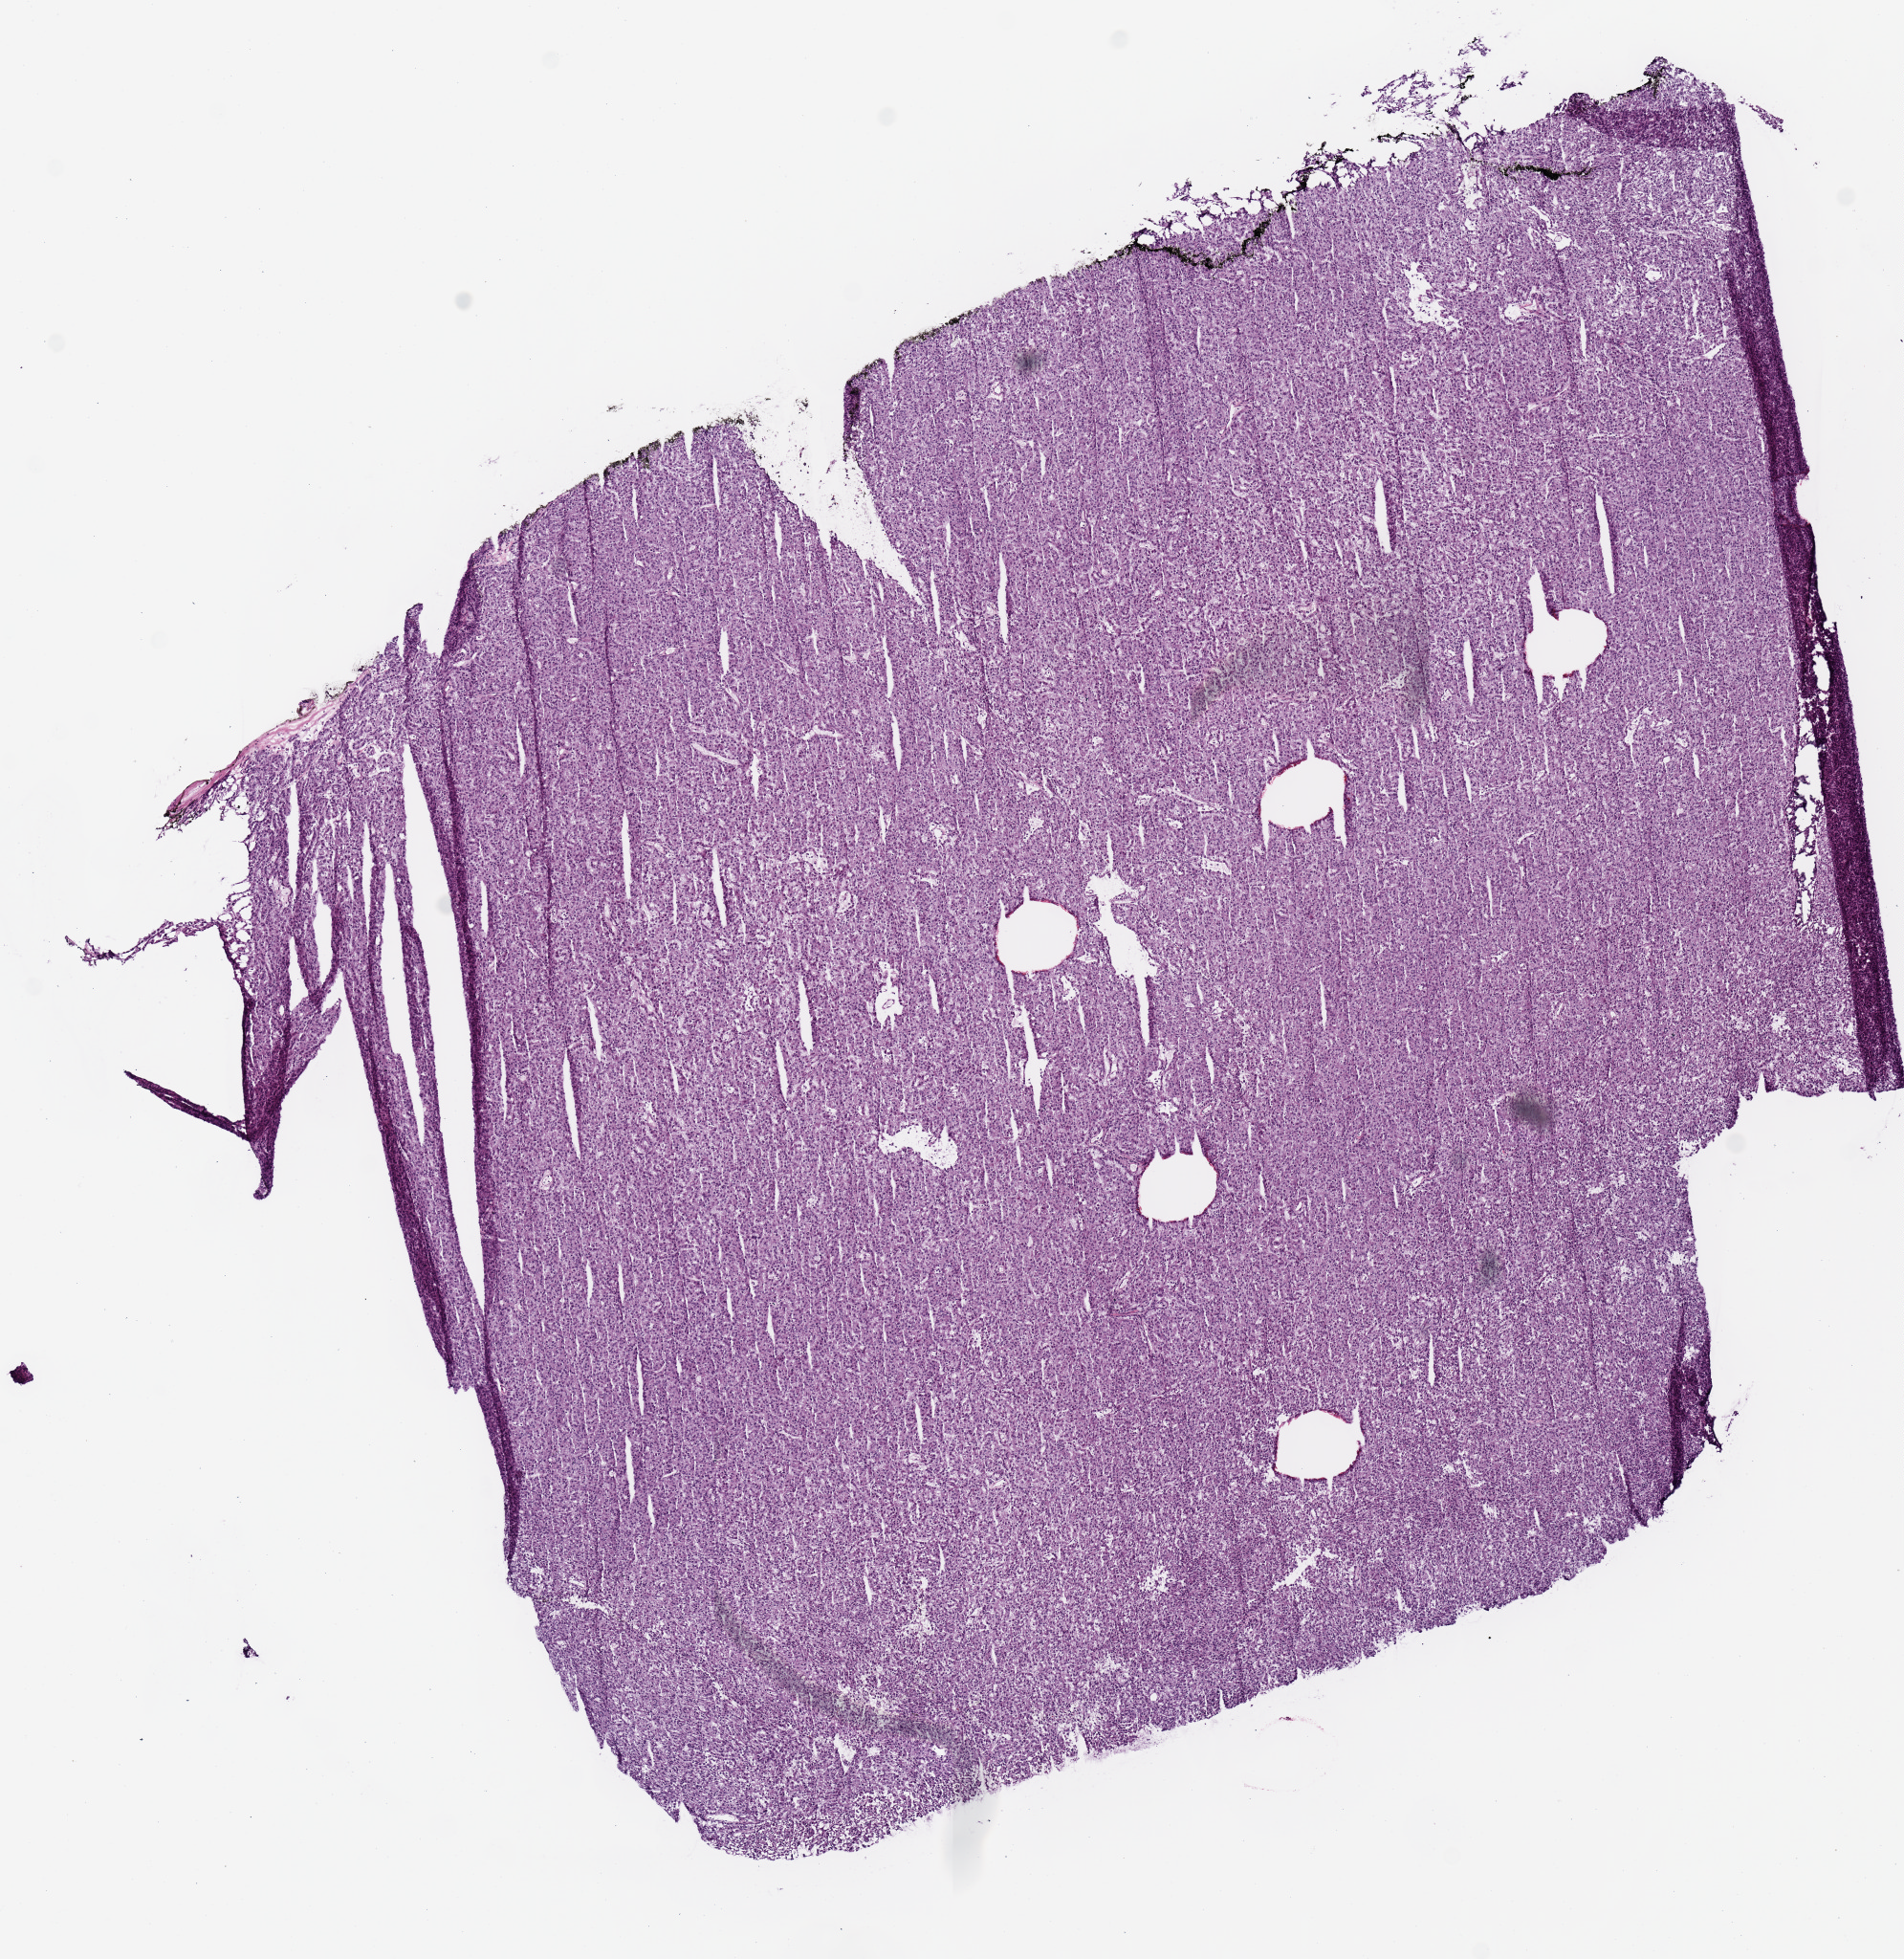
H&E-stained whole-slide image — whole scanned area (about 7.9 x 8.1 mm) shown as a low-resolution overview; frozen section from the top of the tissue portion; primary tumour sample from the kidney. Patient: male, age at initial diagnosis 47 years. Composition of this section per pathologist review: tumour cells 100%, tumour nuclei 90%, normal cells 0%, stromal cells 0%, necrosis 0%. Infiltration values recorded for this section: lymphocyte infiltration 2%, monocyte infiltration 0%, neutrophil infiltration 0%.
AJCC pathologic stage: I (7th edition). TNM: T1a NX MX. Pathologic diagnosis: Papillary adenocarcinoma, NOS.